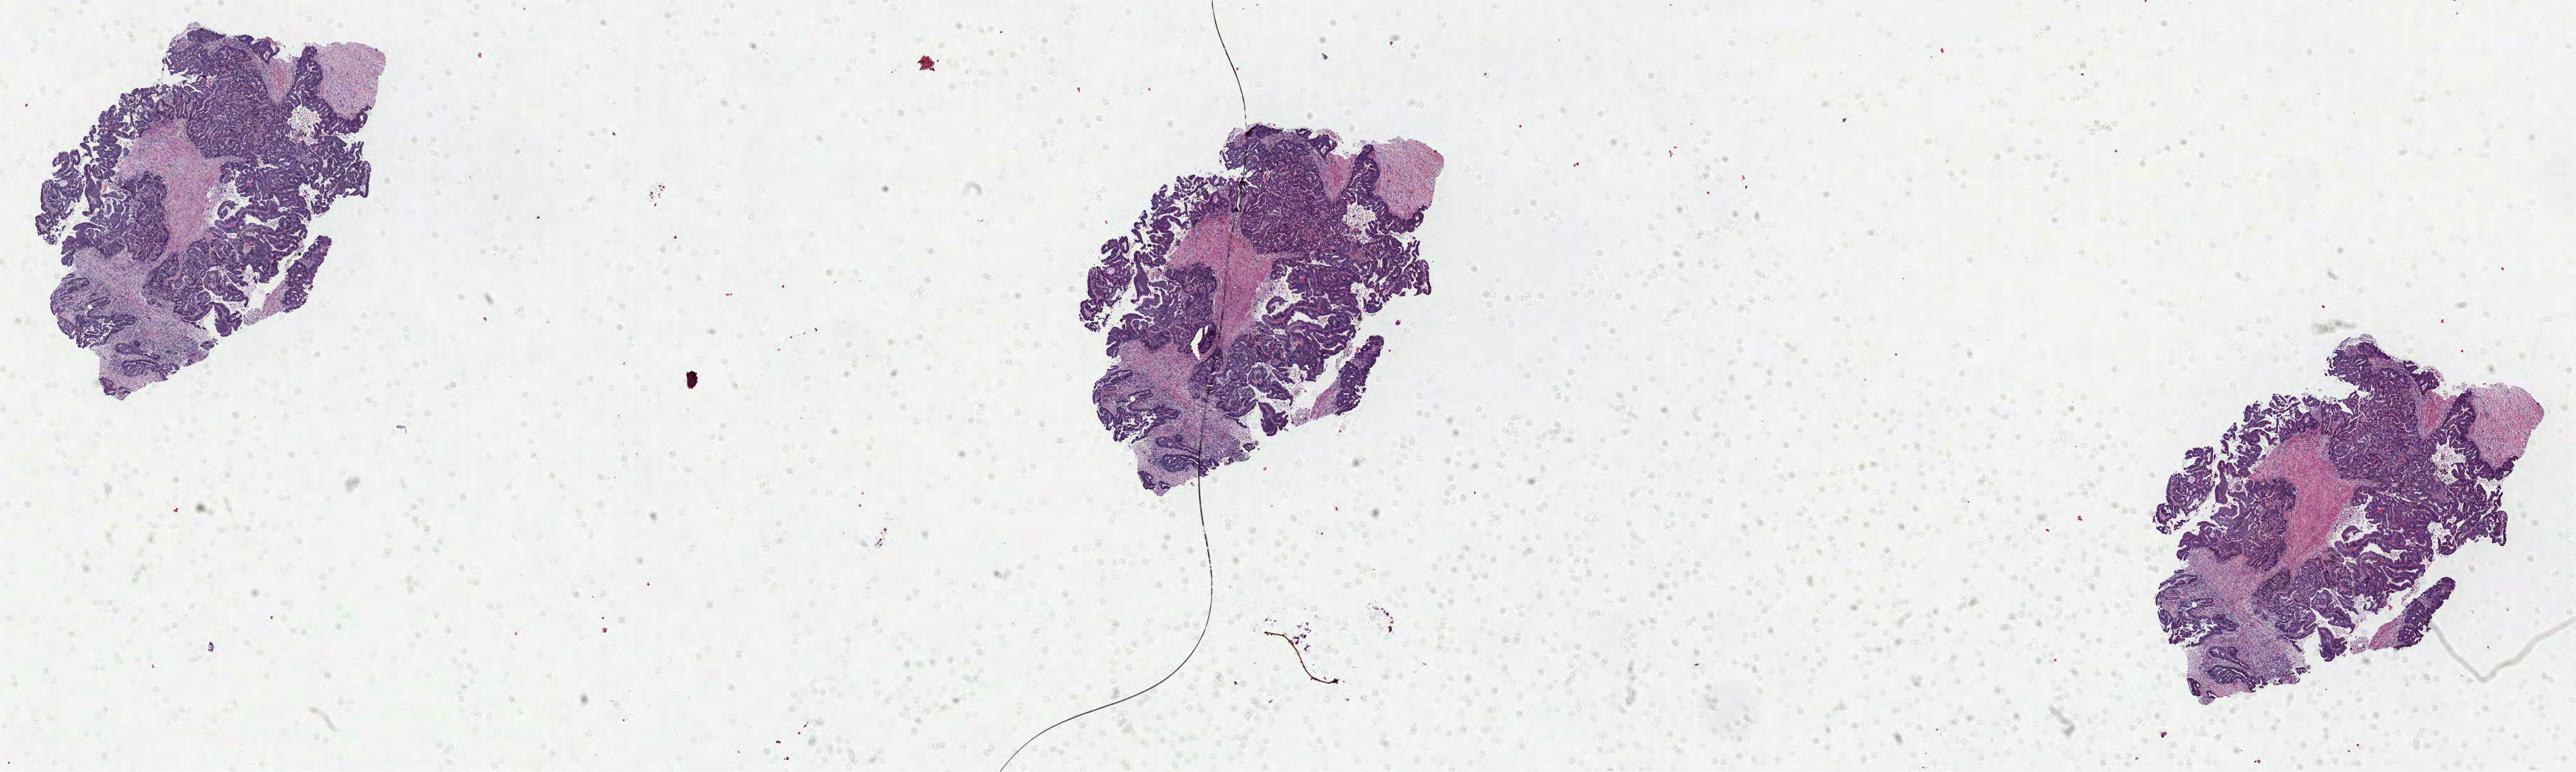
Whole-slide histology image, H&E-stained — shown as a low-resolution overview of the whole scanned area (about 29.5 x 8.8 mm, from a 40x scan), formalin-fixed paraffin-embedded (FFPE) diagnostic section, primary tumour sample from the colon. Male patient; age at initial diagnosis 82 years.
AJCC pathologic stage: I. Lymph nodes positive (case pathology): 0 of 26 examined. Diagnosis: Adenocarcinoma, NOS (ascending colon).